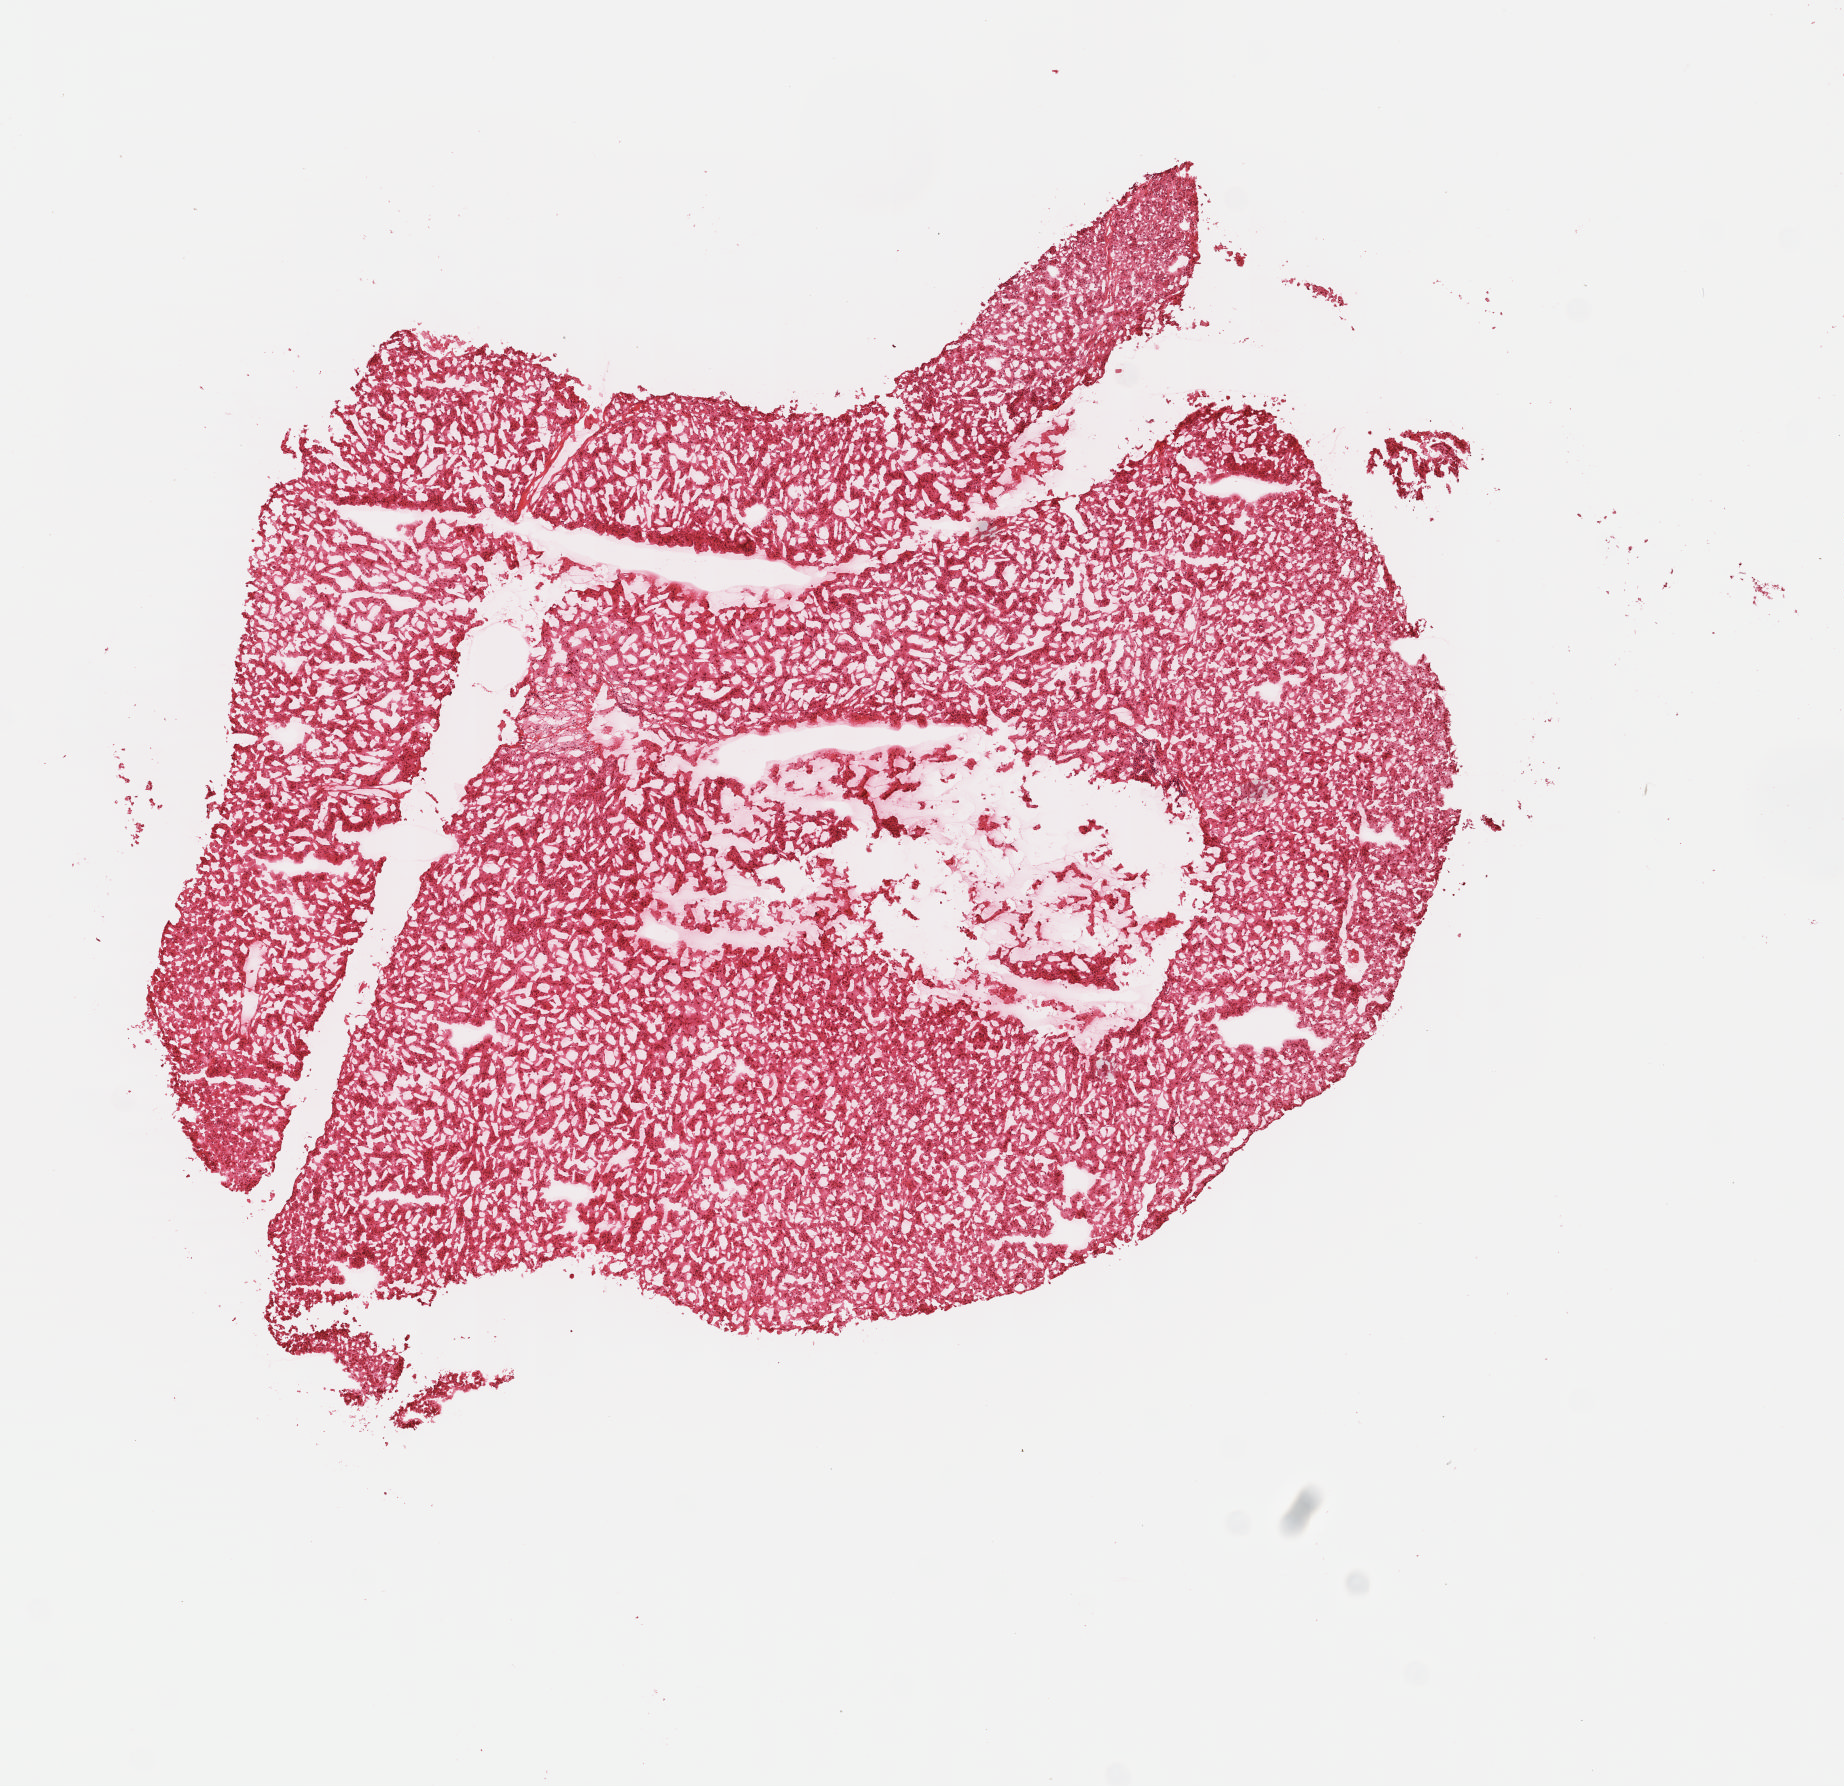
Digitized H&E-stained tissue section (whole slide), shown as a low-resolution overview of the whole scanned area (about 7.2 x 7.0 mm), frozen section, sample: primary tumour, adrenal cortex. Female patient; age at initial diagnosis 53 years. Slide review estimates, as recorded: tumour cells 100%, tumour nuclei 80%.
Diagnosis: Adrenal cortical carcinoma (cortex of adrenal gland).